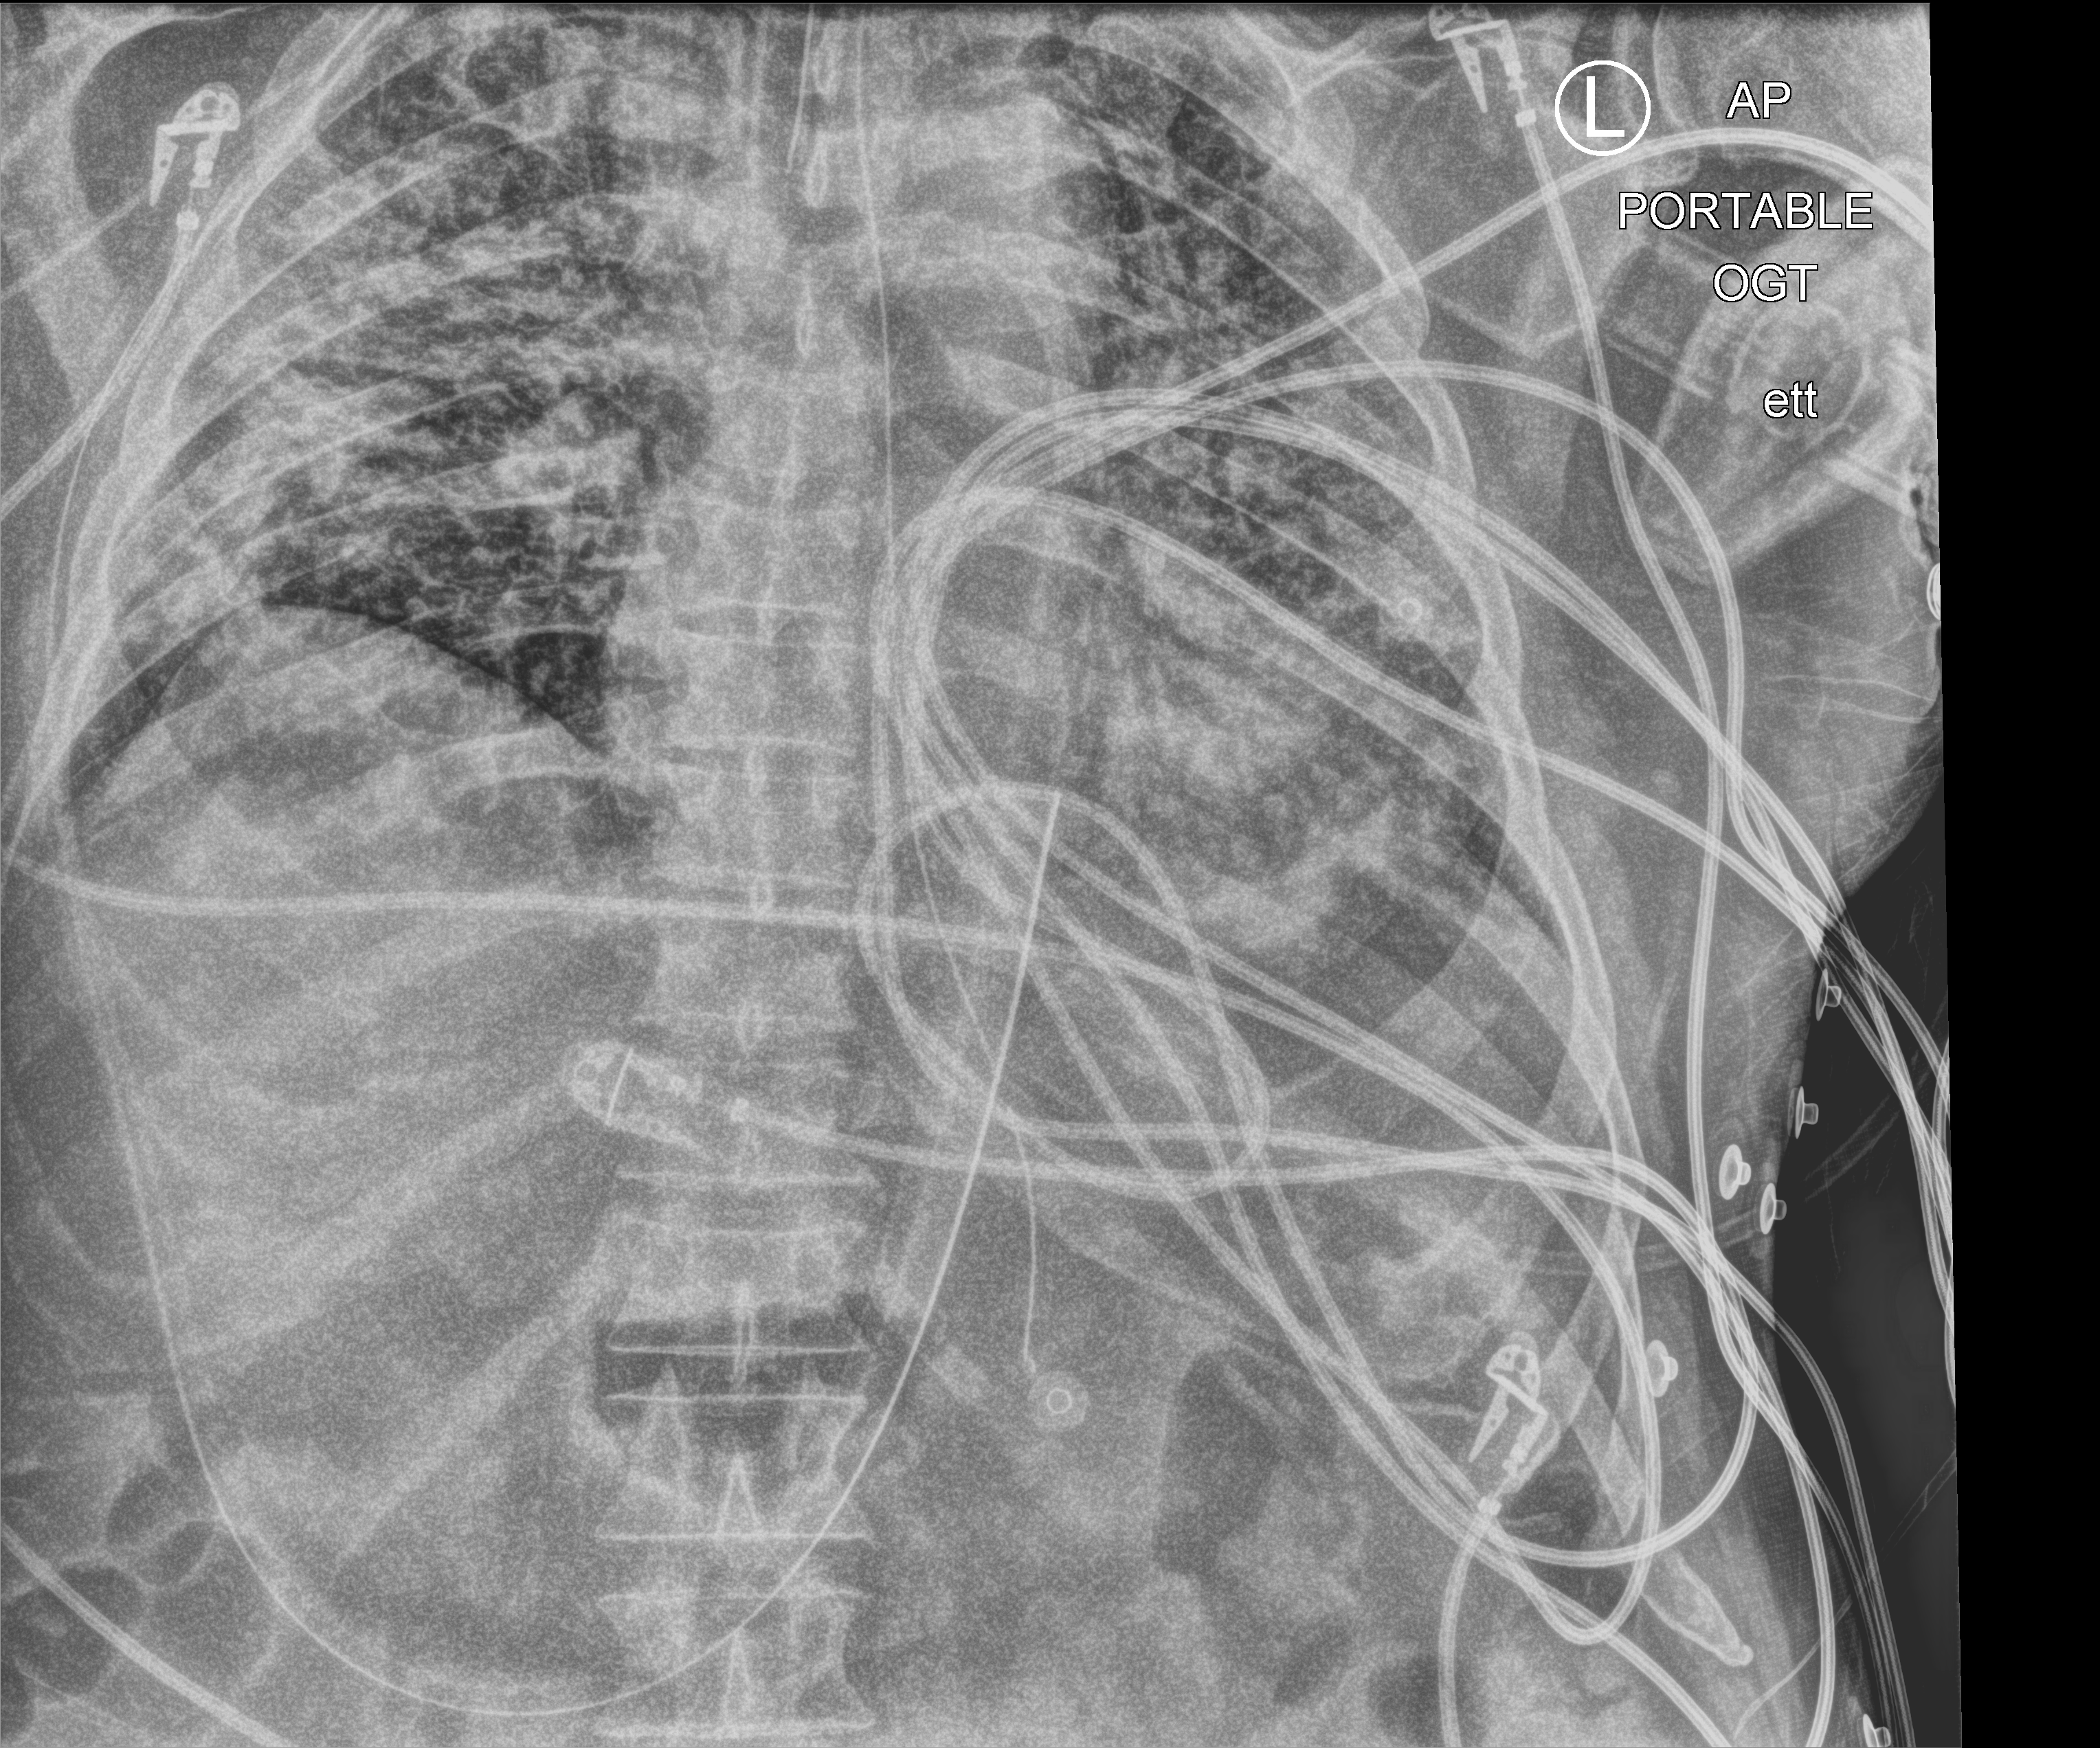
Bedside chest radiograph (computed radiography); anteroposterior (AP) projection. Patient hospitalised with COVID-19; male, aged 60–74 years.
Hospital-stay facts (about this admission, not read from this image; timing relative to this image not recorded): admitted to intensive care during this hospital stay: yes.